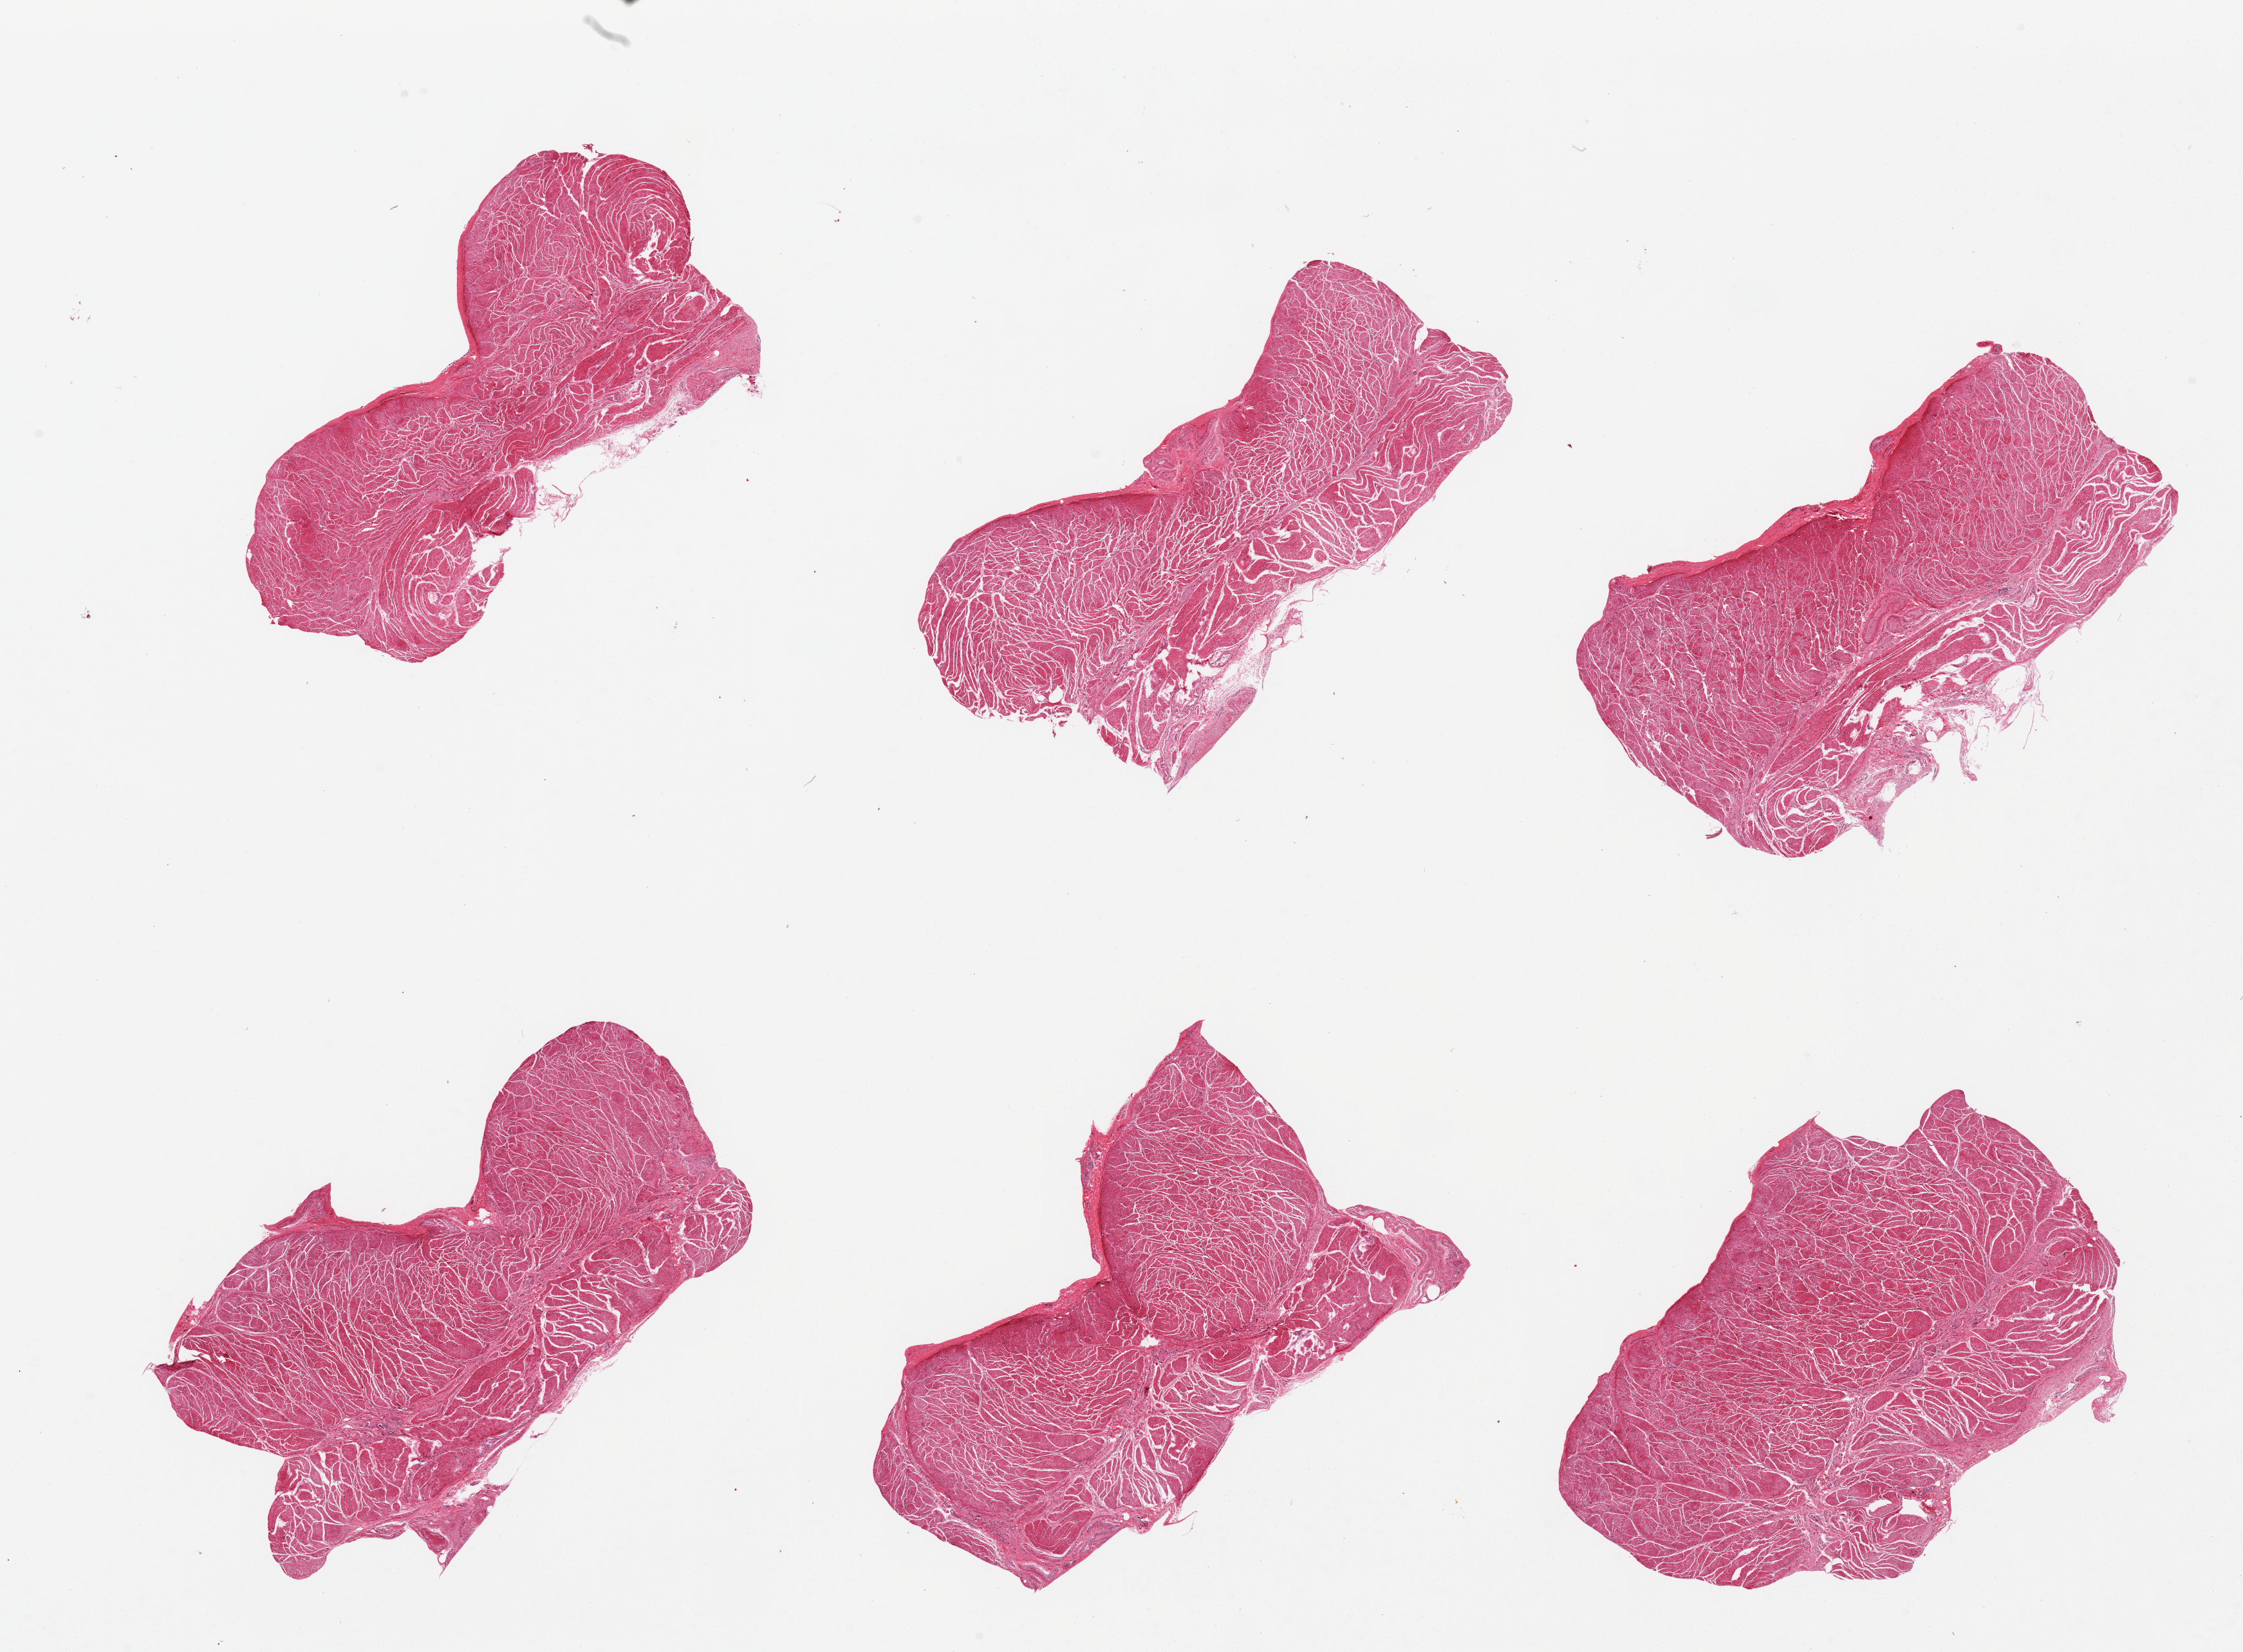
Haematoxylin and eosin whole-slide image — a low-resolution overview of the entire scanned area, about 27.6 x 20.3 mm. PAXgene-fixed, paraffin-embedded tissue. Sampled site (target tissue): gastroesophageal junction. Tissue donor sample. Donor: male.
* reviewer comment on this tissue sample: 6pieces, all muscularis, good specimens